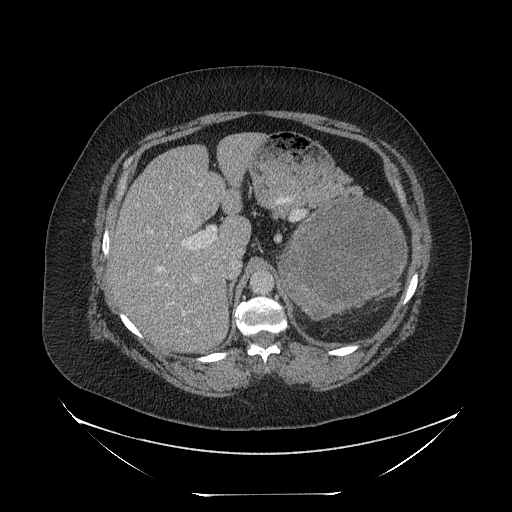
Contrast-enhanced abdominal CT, one axial slice; slice 156 of 205 in the series (ordered by position); reconstruction kernel STANDARD; 120 kVp; intravenous contrast given; soft-tissue window (W 400 / L 40 HU); 2.5 mm slice thickness; 512 × 512 image matrix, field of view 500 × 500 mm. Female patient, age 53 years. From the clinical record (not read from this slice): diagnosis: adrenocortical carcinoma; tumour side: left adrenal; tumour size at pathology: 17 cm; Ki-67 index: 20 %; stage (as recorded): 3.
Outlined on this slice (semi-automatically segmented with operator editing):
- mass: box from (x=282, y=198) to (x=404, y=316) px